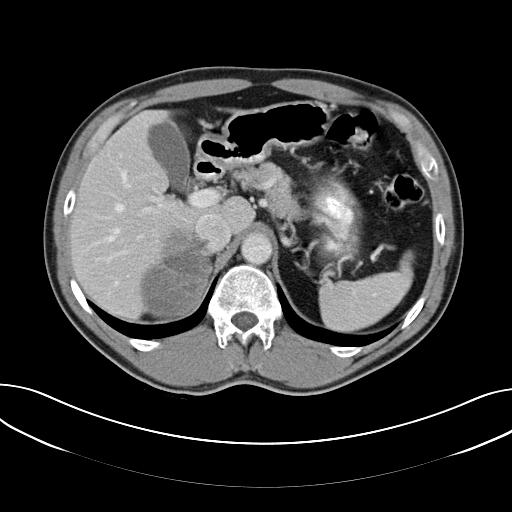
Contrast-enhanced abdominal CT, one axial slice. Position 40 of 61 along the scan axis. Reconstruction kernel B40f. Intravenous contrast given. Soft-tissue window (W 400 / L 40 HU). 5 mm slice thickness. 512 × 512 image matrix, field of view 372 × 372 mm. Patient: male, 57 years. Case-level facts recorded for this patient, not image findings: diagnosis: adrenocortical carcinoma; tumour side: right adrenal; tumour size at pathology: 11.2 cm; Ki-67 index: 10 %; stage (as recorded): 3.
Outlined on this slice (semi-automatically segmented with operator editing):
- mass: bounding box (x1, y1, x2, y2) in pixels: (144, 232, 210, 314)